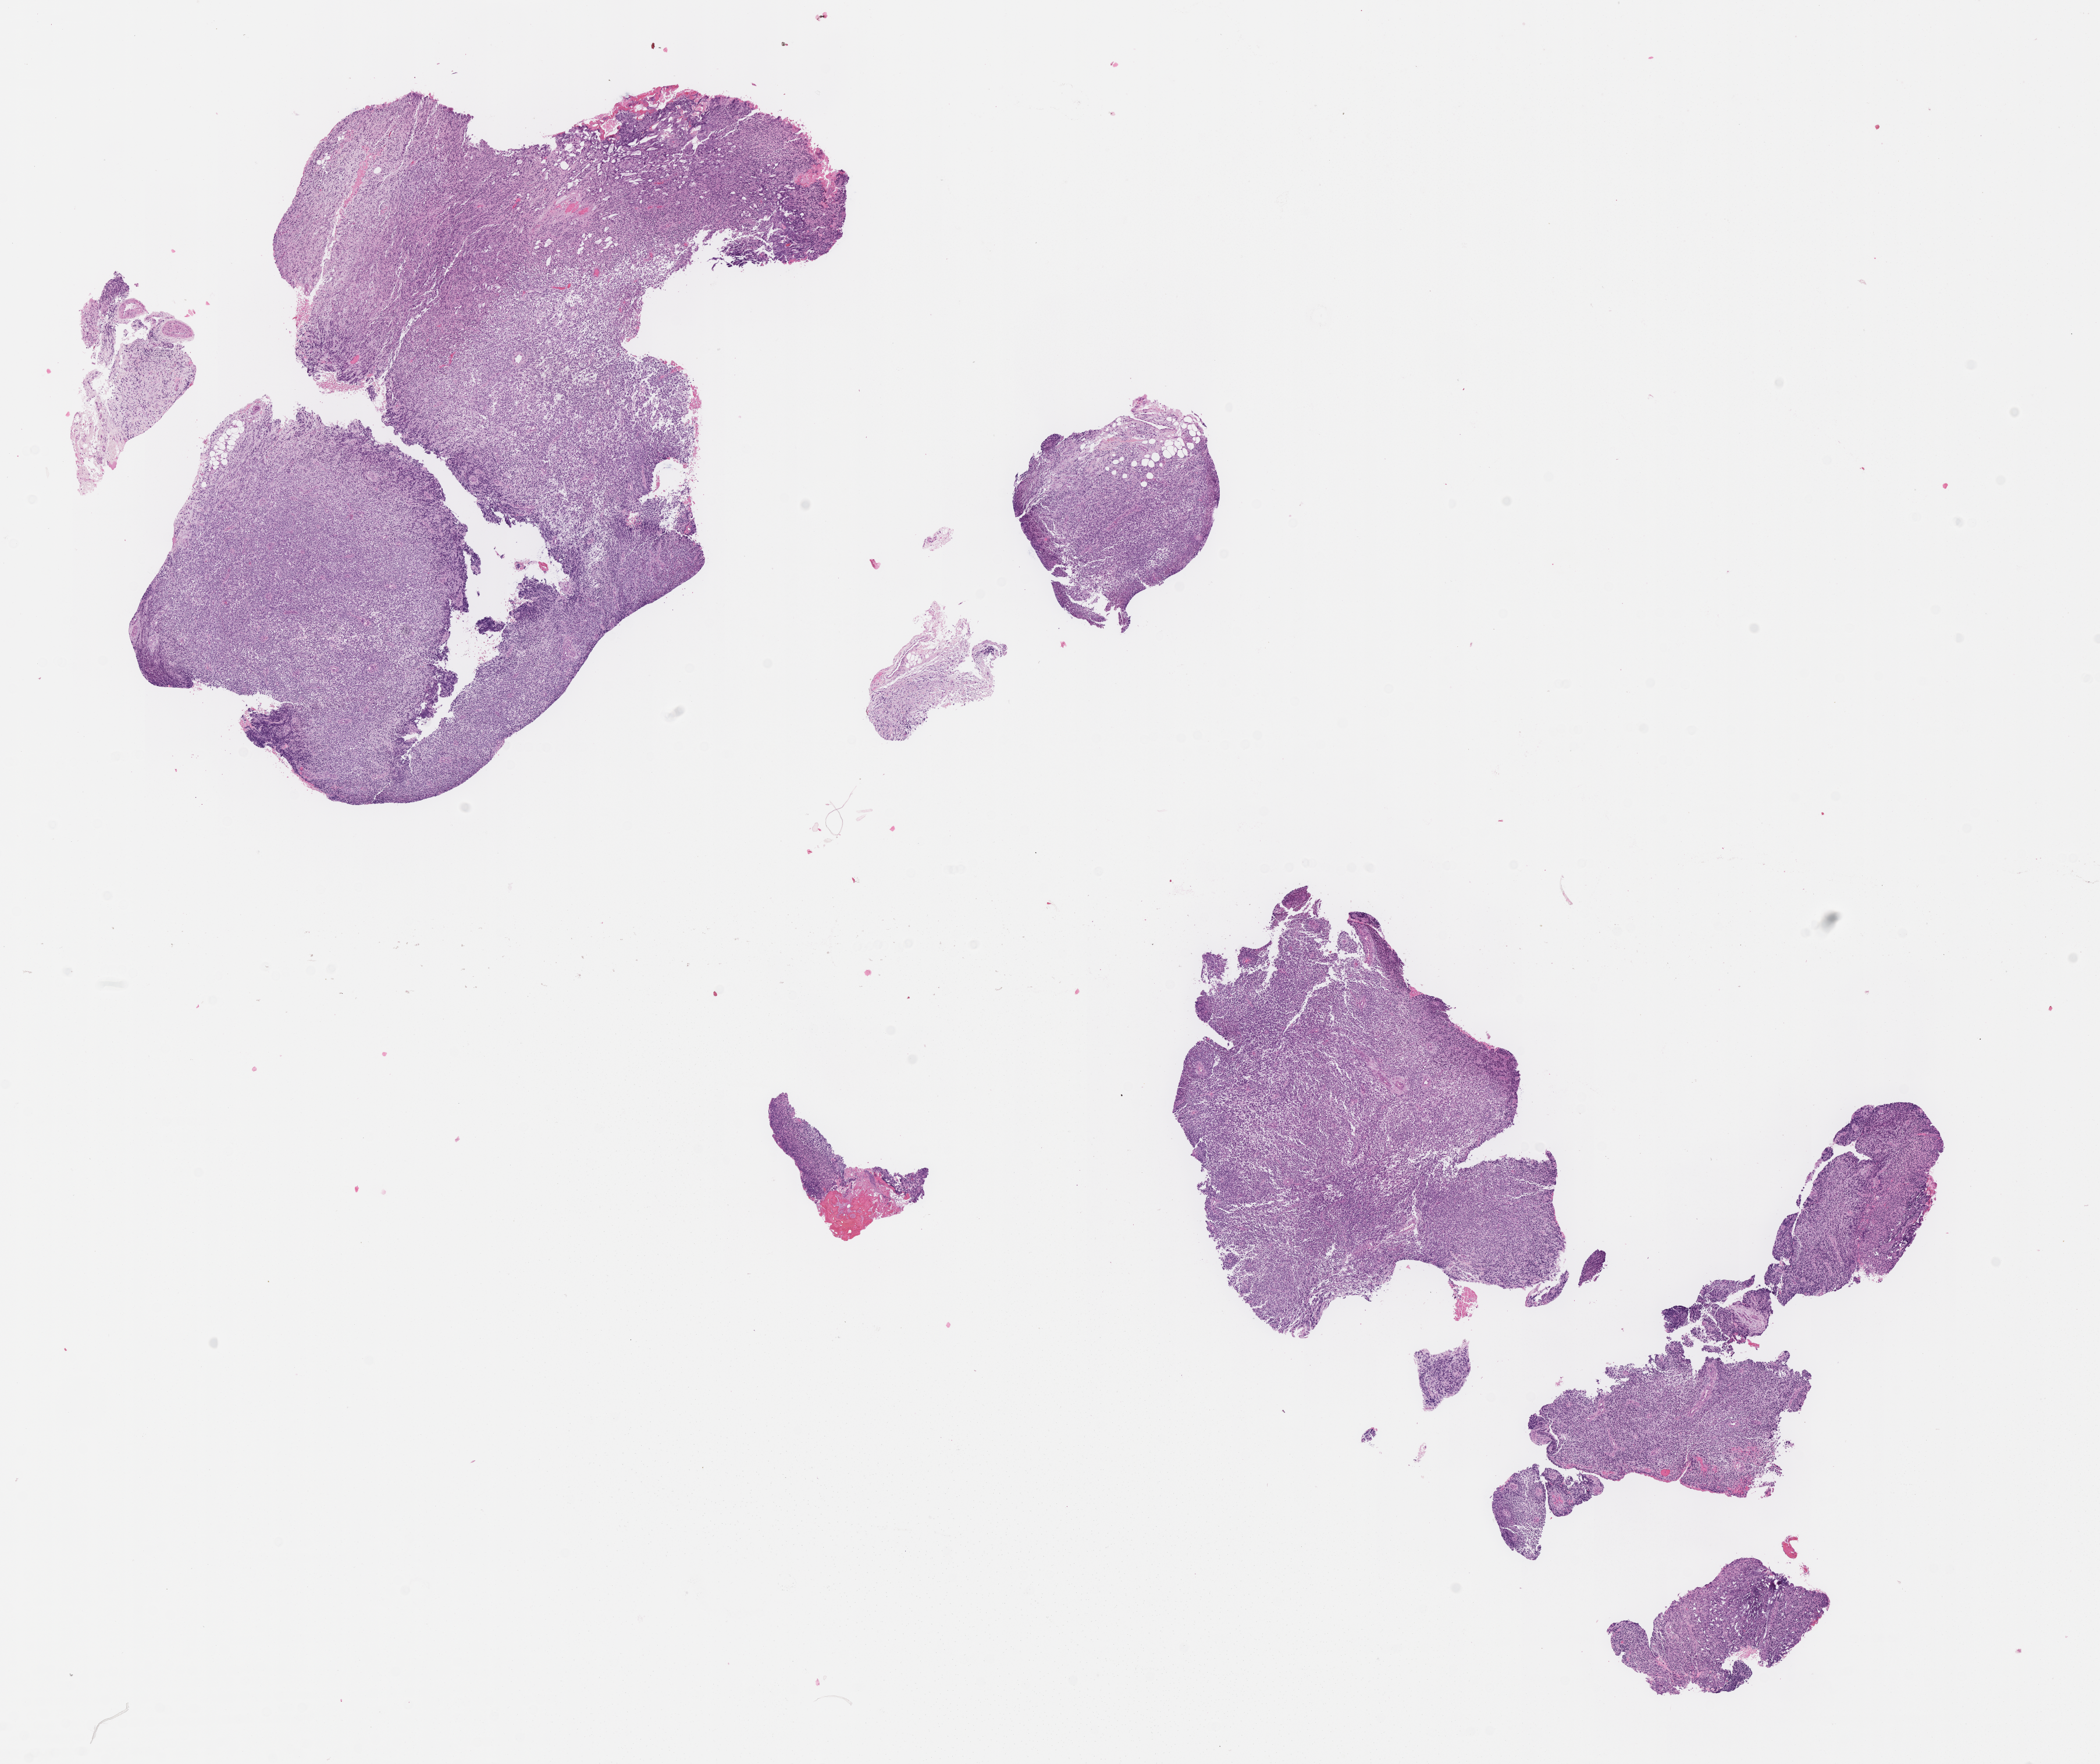
Whole-slide image, H&E stain of tumor tissue, shown as a low-resolution overview of the whole scanned area (about 14.6 x 12.3 mm); FFPE section; sample anatomic site: orbit, right. Female patient, age at diagnosis 6.3 years.
Diagnosis: rhabdomyosarcoma; histological classification: spindle cell rhabdomyosarcoma. Metastatic status at presentation (as recorded): non-metastatic. Stage (as recorded): 1.